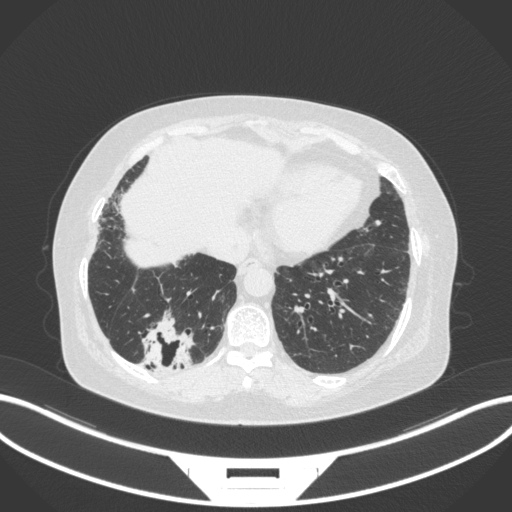
Chest CT, one axial slice; position 51 of 303 along the scan axis; reconstruction kernel B31f; lung window (W 1500 / L -600 HU); 1 mm slice thickness; 512 × 512 image matrix, field of view 400 × 400 mm. Patient: female, 65 years. From the clinical record (not read from this slice): clinical TNM (as recorded): T2b N1 M0.
Annotated regions visible in this slice (bounding box drawn by a radiologist):
- lung tumour (recorded histology: adenocarcinoma): bounding box (x1, y1, x2, y2) in pixels: (133, 306, 196, 375)